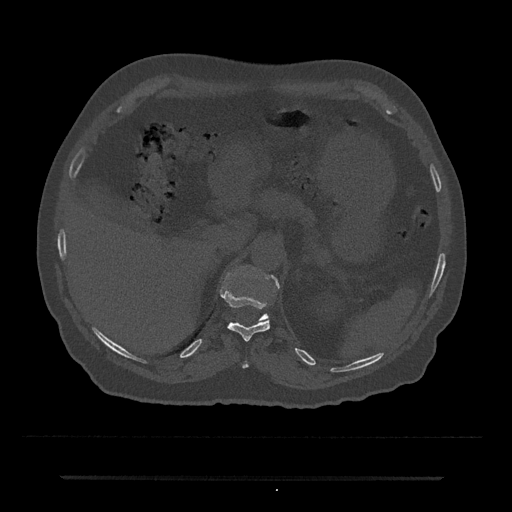
CT including the spine, one axial slice. Position 172 of 797 along the scan axis. Reconstruction kernel Br40s/3. Bone window (W 1800 / L 400 HU). 512 × 512 image matrix, field of view 437 × 437 mm. Patient: male, 69 years. From the clinical record (not read from this slice): primary cancer: prostate.
Outlined on this slice (semi-automatically segmented with operator editing):
- T10 vertebra: box from (x=242, y=360) to (x=249, y=369) px
- T11 vertebra: (x=221, y=291)–(x=270, y=341)
- T12 vertebra: (x=260, y=275)–(x=279, y=320)